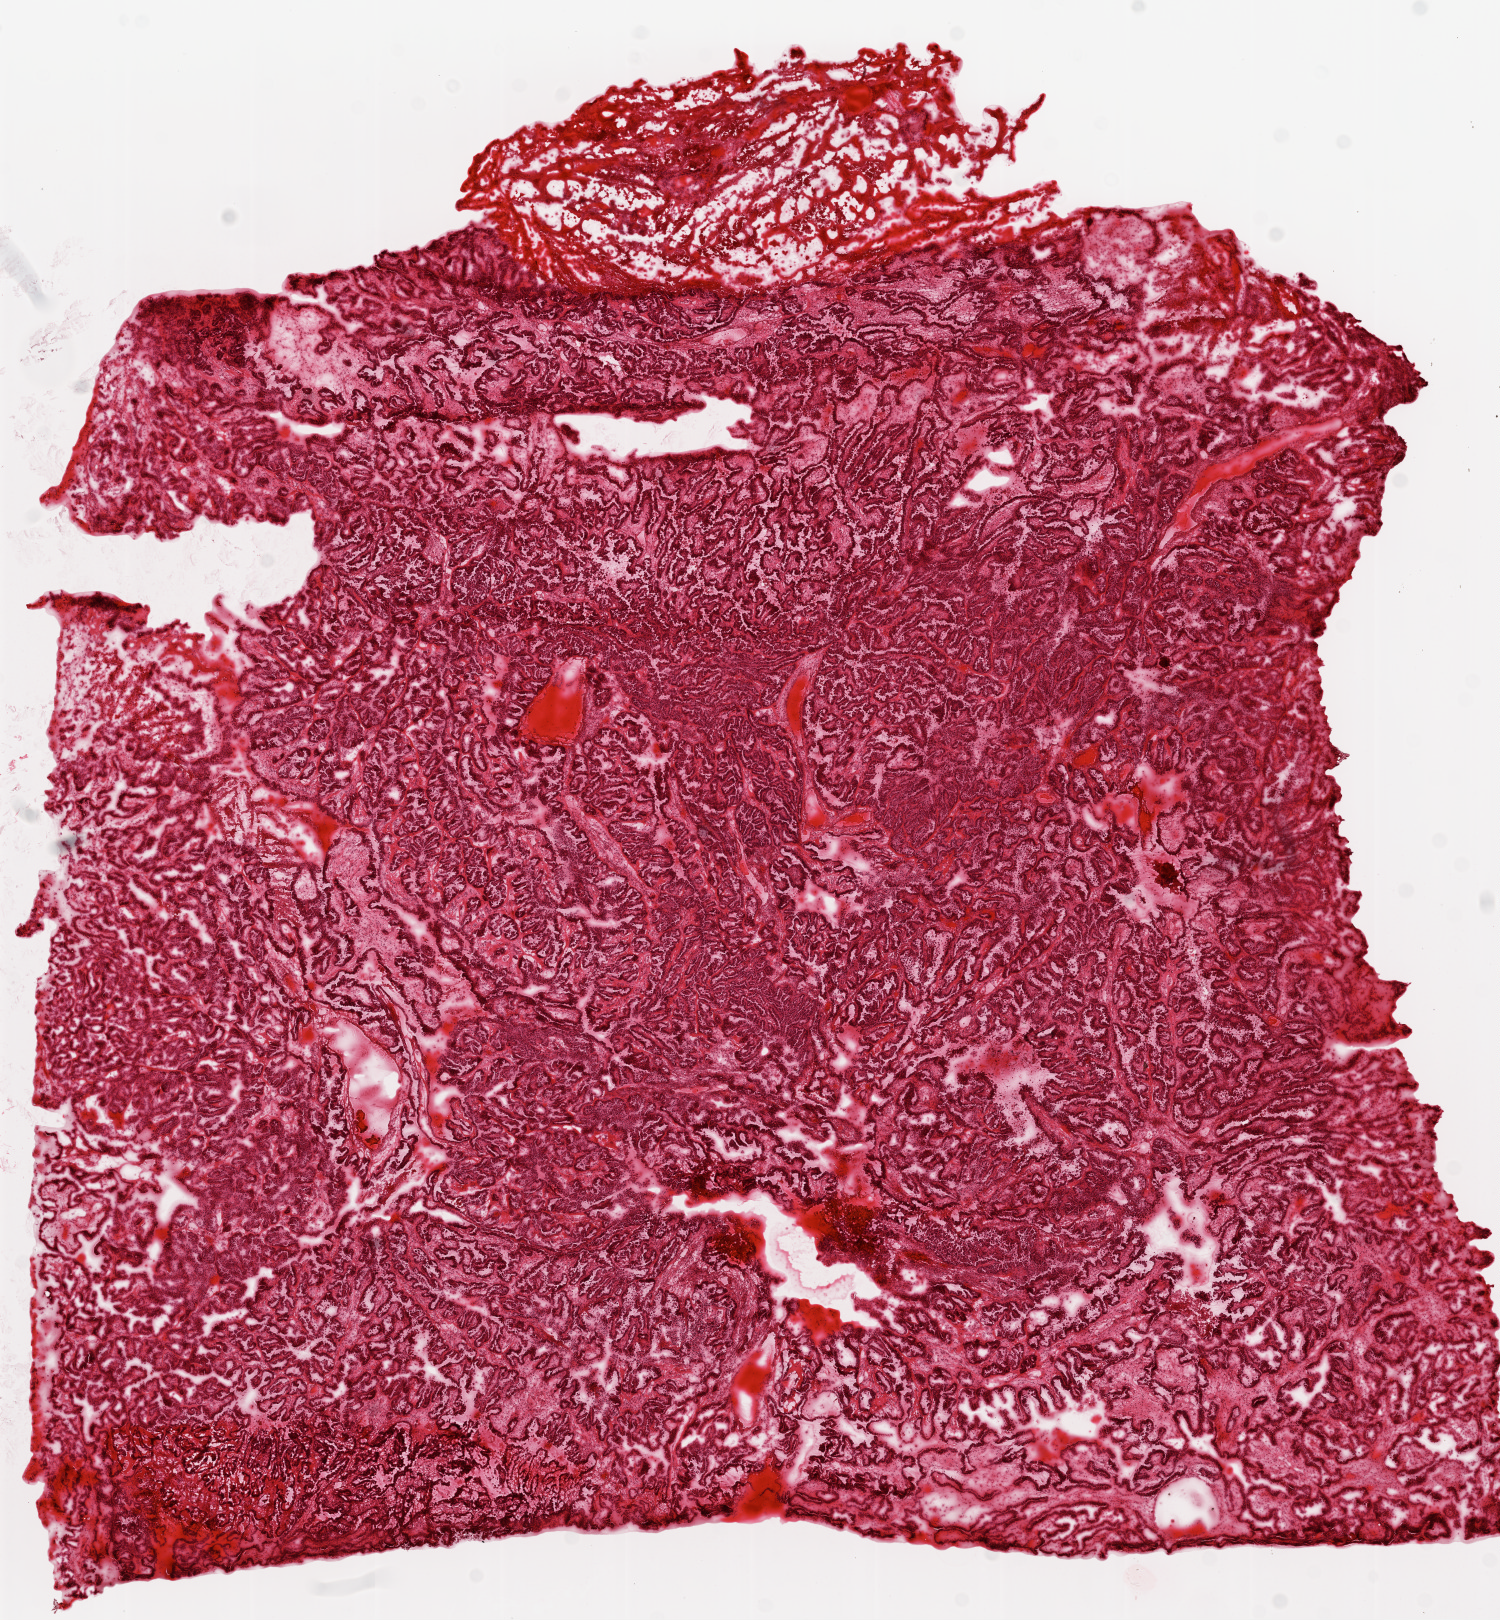
Digitized Hematoxylin and eosin (H&E) stained tissue section (whole slide) — low-resolution overview of the scanned area, about 12.0 x 13.0 mm, frozen section from the top of the tissue portion, ovary, primary tumour sample. Female, age 51 years at initial diagnosis. Histologic grade: G3 (poorly differentiated). Composition of this section per pathologist review: tumour cells 95%, tumour nuclei 95%, normal cells 0%, stromal cells 4%, necrosis 1%.
Histologic diagnosis: Serous cystadenocarcinoma, NOS. FIGO stage: IIIC. Laterality: right.